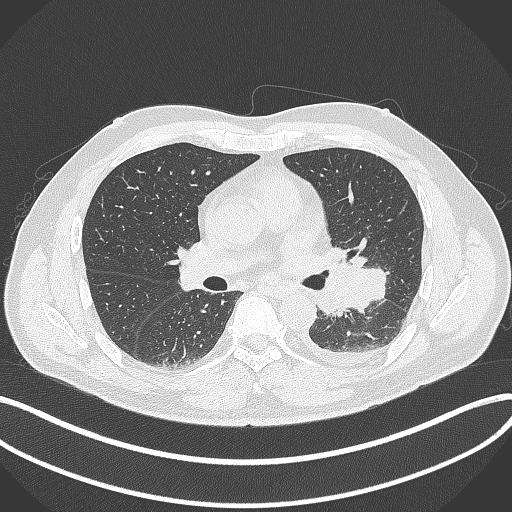
Chest CT, one axial slice. Lung window (W 1500 / L -600 HU). 1 mm slice thickness. 512 × 512 image matrix, field of view 400 × 400 mm. Patient: male, 58 years. From the clinical record (not read from this slice): clinical TNM (as recorded): T3 N1 M1b; histopathological grade: G3.
Outlined on this slice (bounding box drawn by a radiologist):
- lung tumour (recorded histology: small cell carcinoma): bounding box (x1, y1, x2, y2) in pixels: (314, 256, 394, 319)